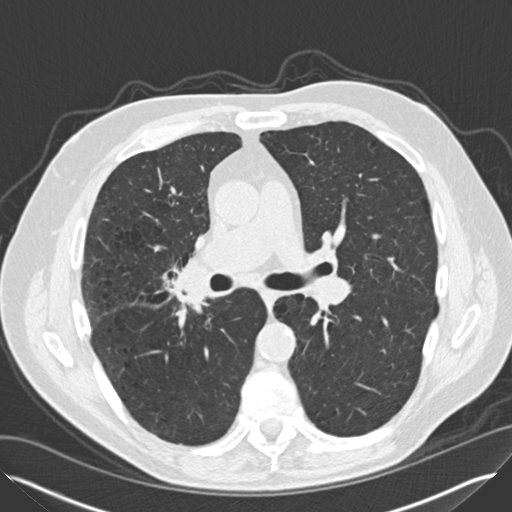
Low-dose screening chest CT, one axial slice. Slice 82 of 149 in the series (ordered by position). Reconstruction kernel B30f. Lung window (W 1500 / L -600 HU). 2 mm slice thickness. 512 × 512 image matrix, field of view 370 × 370 mm.
Annotated regions visible in this slice (outlined manually by an expert reader):
- lesion 2 (tumor, hilum of right lung): bounding box <181,256,210,302> (left, top, right, bottom; pixels)